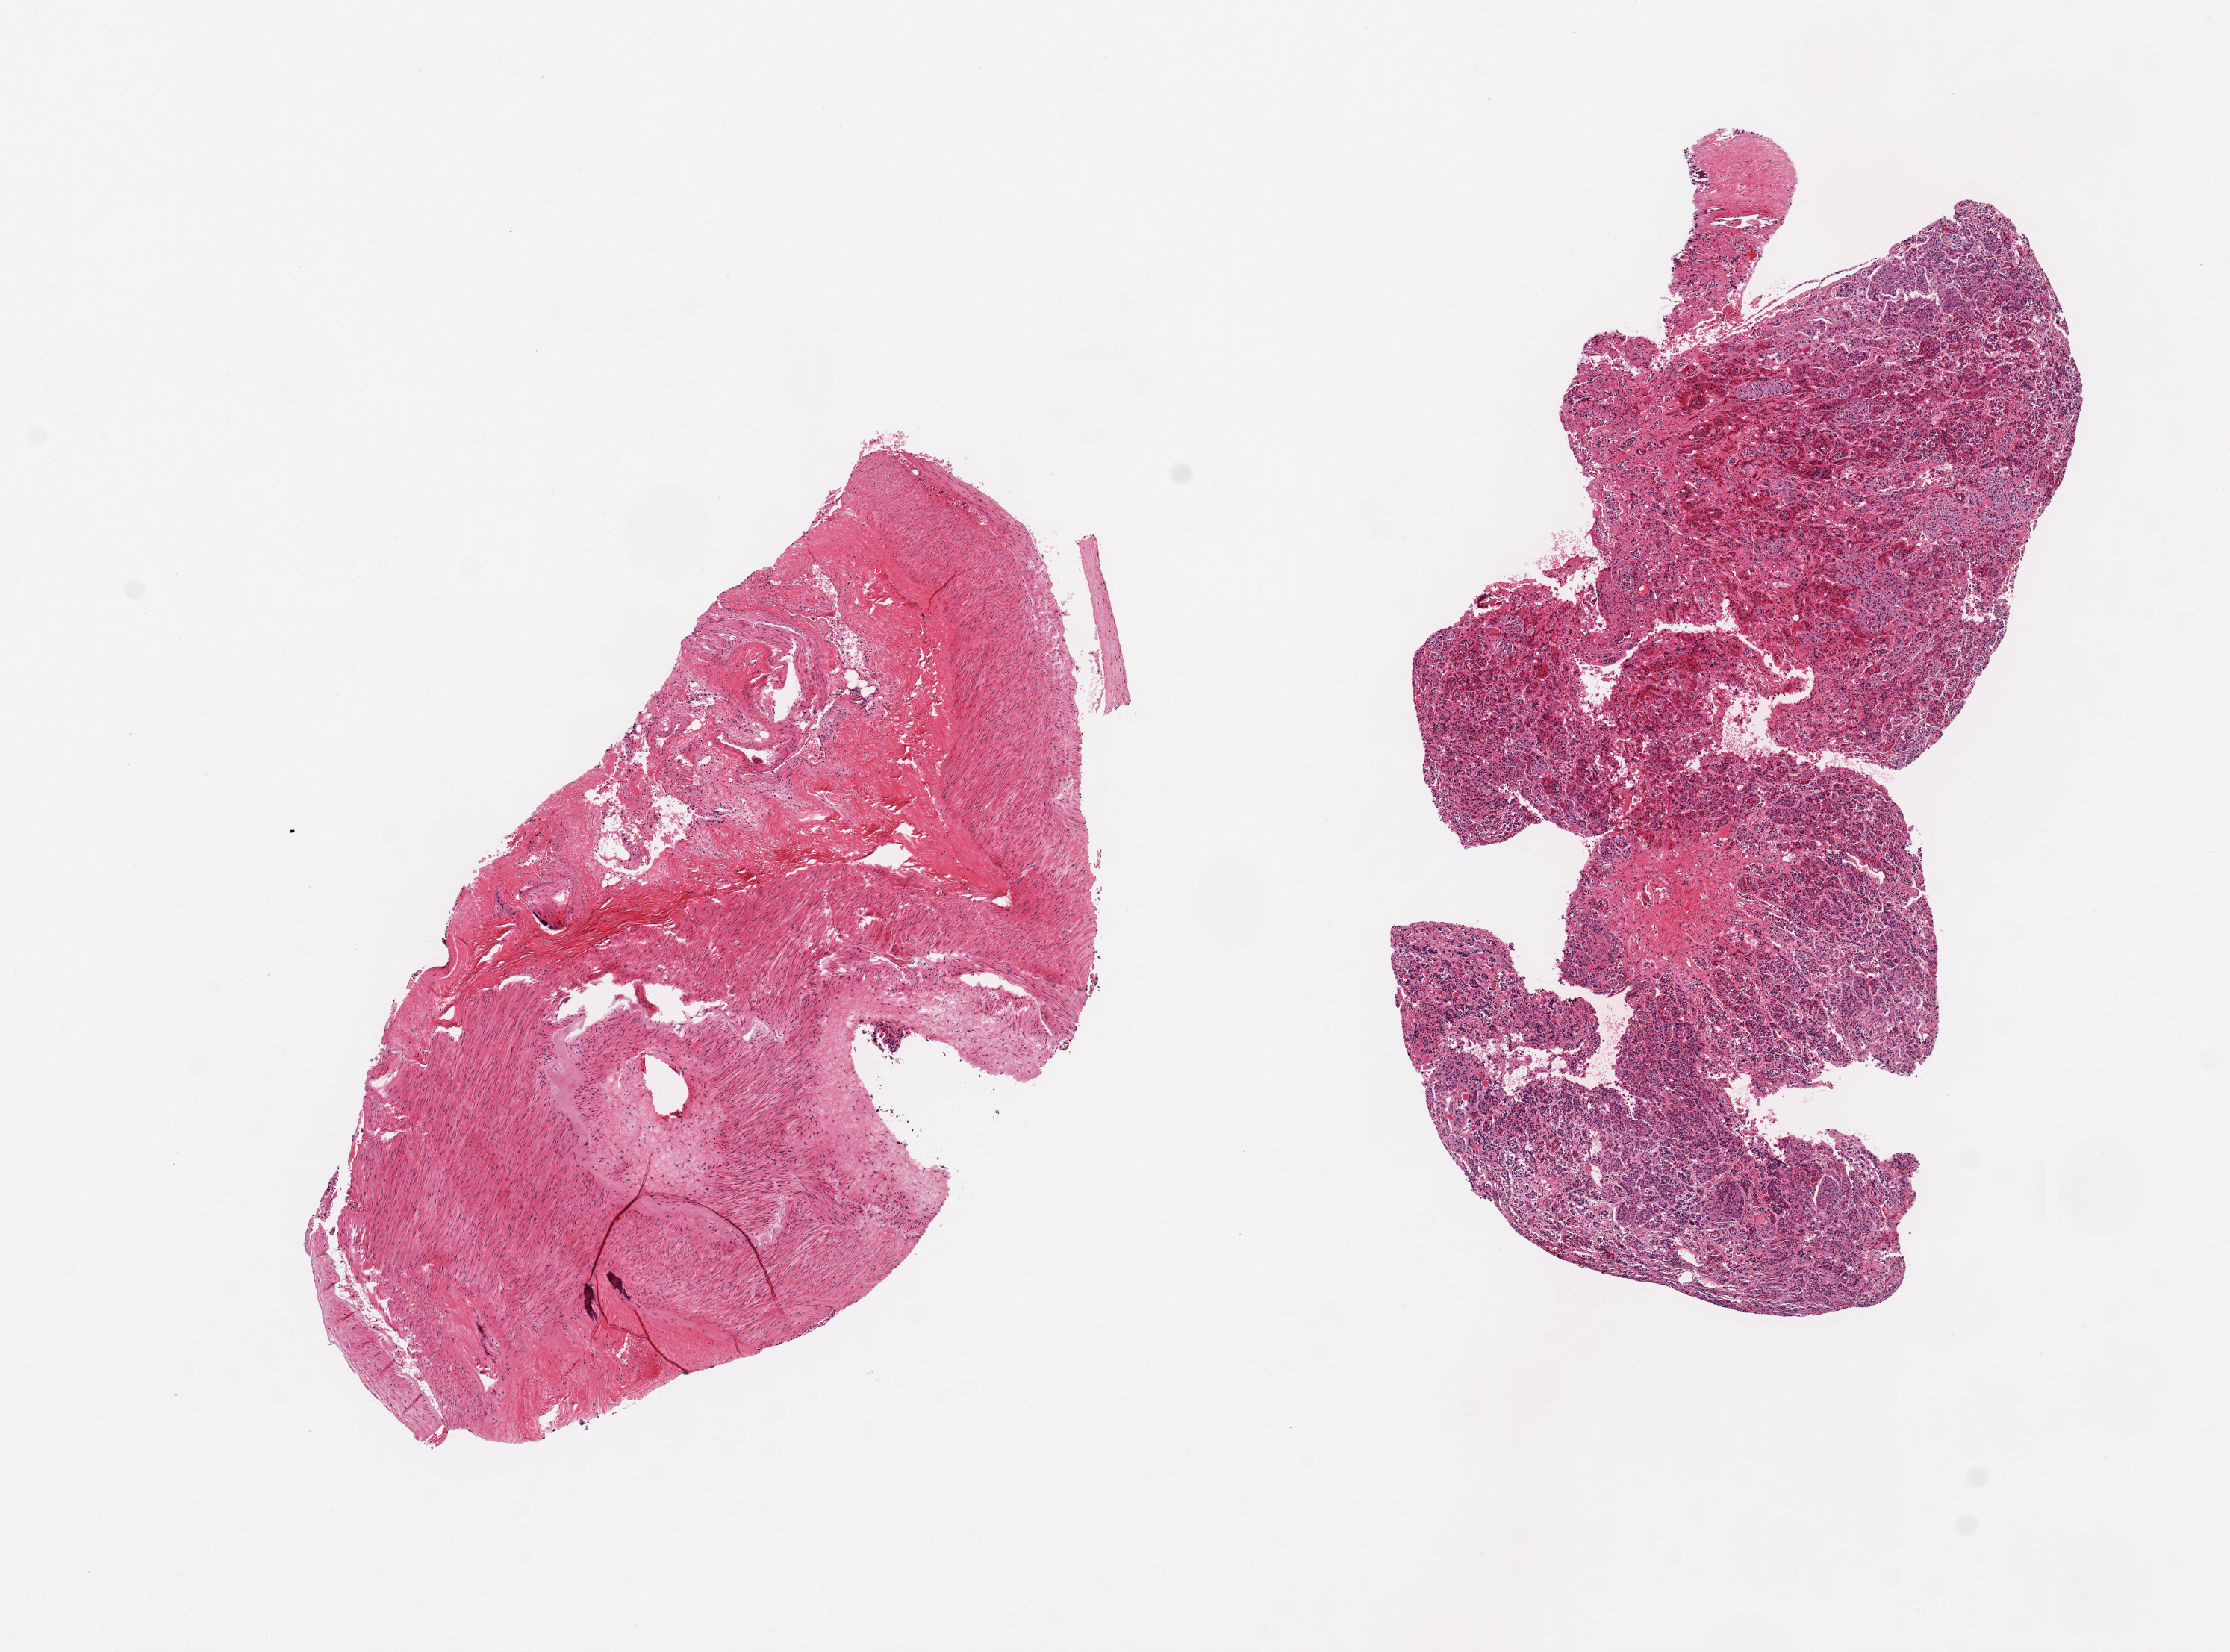
Digitized H&E-stained section, brightfield, low-resolution overview of the scanned area, about 11.8 x 8.8 mm (from a 20x scan); PAXgene-fixed paraffin-embedded (PFPE) section; sampled site (target tissue): pituitary; tissue donor sample. Donor: male.
* reviewer comment on this tissue sample: 2 pieces, one adenohypophysis; one extra fragment of dura--ignore